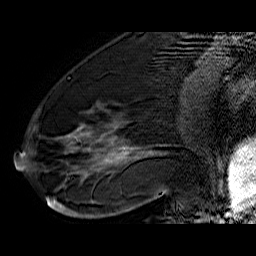
Breast MRI (dynamic contrast-enhanced), one sagittal slice; slice 23 of 60 in the series (ordered by position); dynamic contrast-enhanced series, time point 2 of 6 at this slice position (early post-contrast); 1.5 T; TE 6.4 ms, TR 32.9 ms; 4 mm slice thickness; 256 × 256 image matrix, field of view 200 × 200 mm. Female patient. Case-level facts recorded for this patient, not image findings: setting: breast cancer imaged before/during neoadjuvant chemotherapy; receptor status: HR-positive, HER2-negative.
Annotated regions visible in this slice (semi-automatically segmented with operator editing):
- analysis volume of interest (the breast-tissue region the enhancement analysis was run in; not a lesion): bounding box [x1, y1, x2, y2] px = [45, 74, 176, 210]
- tumour enhancement mask (voxels above the 100 % enhancement threshold inside the analysis volume of interest): [46, 125, 157, 209]